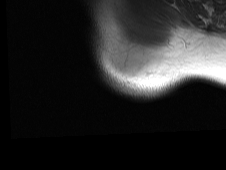
MRI of an extremity soft-tissue mass, one axial slice; slice 61 of 81 in the series (ordered by position); MR volume resampled by the dataset authors to the PET/CT grid (not the native acquisition matrix); 3.27 mm slice thickness; 226 × 170 image matrix, field of view 221 × 166 mm. Male patient. From the clinical record (not read from this slice): histological type: pleiomorphic spindle cell undifferentiated; grade: high; site of the primary tumour: right parascapusular.
Outlined on this slice (expert contour drawn on MRI and transferred to this co-registered scan by the dataset authors):
- gross tumour volume including surrounding oedema: bounding box (x1, y1, x2, y2) in pixels: (113, 56, 161, 82)
- gross tumour volume (mass): (115, 56, 134, 78)